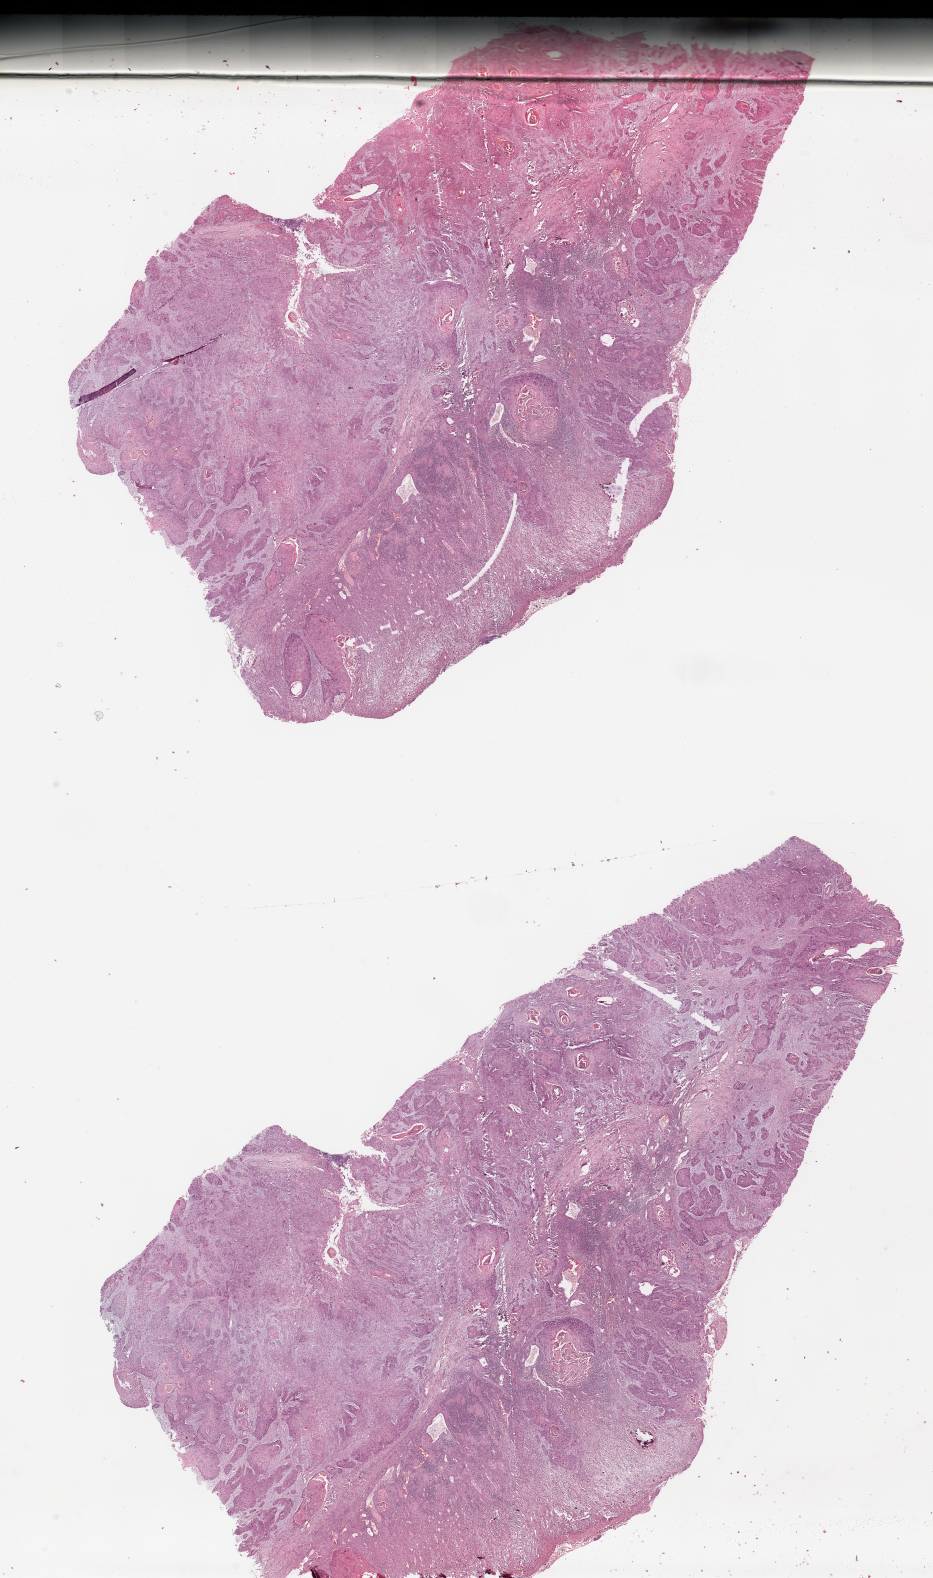
H&E whole-slide image, a low-resolution overview of the entire scanned area, about 14.8 x 25.0 mm (slide scanned at 20x), tumour tissue sample, sampled site: sinus. Patient: male, age 64 years. Histologic grade: G2 (moderately differentiated). Composition of this section per pathologist review: tumour nuclei 80%, necrosis 3%.
Primary tumour site (as recorded): hypopharynx. Diagnosis: Squamous cell carcinoma, NOS (head, face or neck, NOS). AJCC pathologic stage: III.